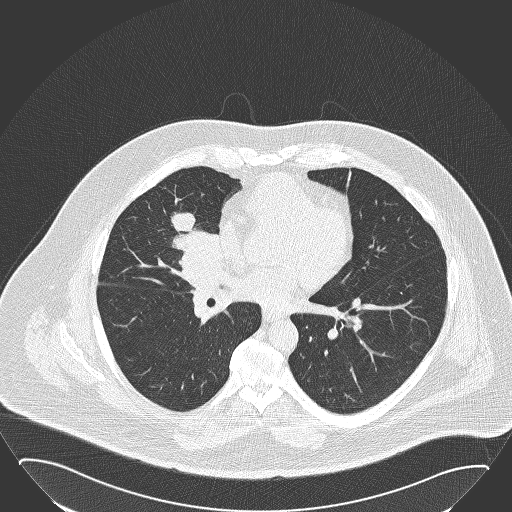
Low-dose screening chest CT, axial slice, first (baseline) screen, lung window (W 1500 / L -600 HU), 2 mm slice thickness, lung (sharp) reconstruction kernel (B50f). Male, age 61 years at enrolment. Former smoker at enrolment.
Expert reader's lesion annotation, bounding box <145,201,230,287> (left, top, right, bottom; pixels). The screening reader recorded 2 non-calcified nodules or masses ≥4 mm on this exam (right middle lobe, left lower lobe); which of them this box marks is not recorded.